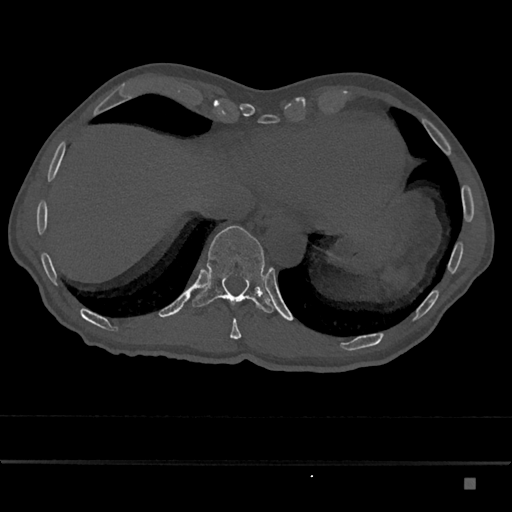
CT including the spine, one axial slice. Slice 695 of 797 in the series (ordered by position). Bone window (W 1800 / L 400 HU). 512 × 512 image matrix, field of view 390 × 390 mm. Patient: male, 72 years. Case-level facts recorded for this patient, not image findings: primary cancer: prostate.
Structures marked on this image (semi-automatic segmentation, software-assisted and operator-edited):
- T10 vertebra: box from (x=230, y=319) to (x=242, y=339) px
- T11 vertebra: (x=192, y=225)–(x=274, y=313)